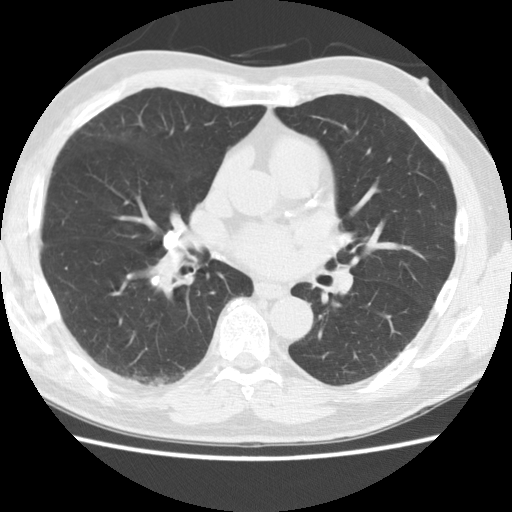
Axial slice from a low-dose chest CT screening exam, first (baseline) screen, lung window (W 1500 / L -600 HU), 2.5 mm slice thickness, standard (soft-tissue) reconstruction kernel (STANDARD), 120 kVp, slice 67 of 116 in the series, 512 × 512 image matrix, field of view 340 × 340 mm. Male participant, aged 66 years at enrolment. Current smoker at enrolment.
Lesion marked by an expert reader, bounding box [x1, y1, x2, y2] px = [145, 213, 203, 263]. No non-calcified nodule or mass ≥4 mm was recorded by the screening reader at this exam. Official screen result: negative screen, no significant abnormalities. Later outcome: lung cancer diagnosed 314 days after this screen — large cell neuroendocrine carcinoma, right middle lobe, poorly differentiated (G3), stage IIIA (AJCC 6th edition), 15 mm at pathology.